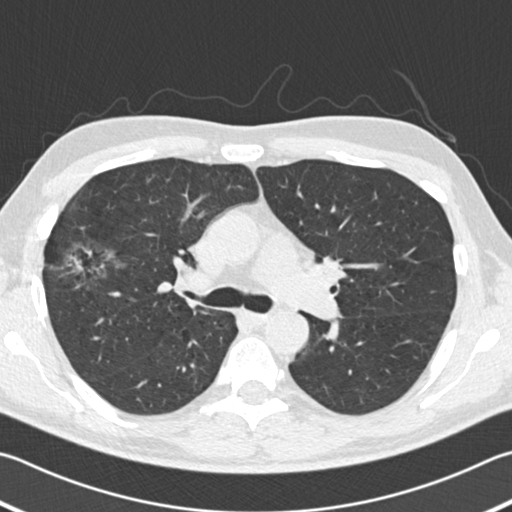
Chest CT (low-dose screening protocol), one axial image, second annual screen, lung window (W 1500 / L -600 HU), 2 mm slice thickness, standard (soft-tissue) reconstruction kernel (B30f), 120 kVp, slice 65 of 182 in the series. Male, age 56 years at enrolment.
Expert-annotated lung lesion, box from (x=46, y=232) to (x=127, y=297) px. Reader record for this screening exam (exam-level; its link to the box is not recorded): non-calcified nodule or mass ≥4 mm, right upper lobe, 18 × 14 mm, spiculated (stellate) margins, soft tissue attenuation, pre-existing on the prior screen: yes; interval growth: yes.